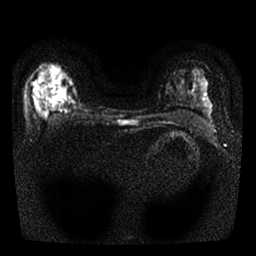
Breast MRI, one axial slice; position 18 of 25 along the scan axis; diffusion-weighted series; image 2 of 4 stored at this slice position (different b-values; order by instance number); 1.5 T; 4 mm slice thickness; 256 × 256 image matrix, field of view 300 × 300 mm. Female patient.
Structures marked on this image (manually delineated by an expert):
- tumour on diffusion-weighted imaging: bounding box [x1, y1, x2, y2] px = [35, 102, 47, 118]